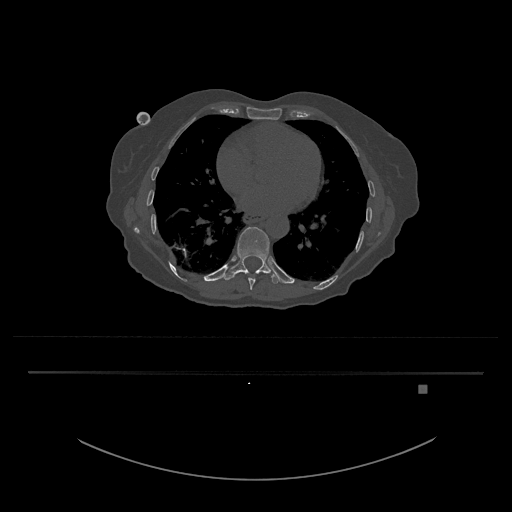
CT including the spine, one axial slice; position 730 of 797 along the scan axis; reconstruction kernel Br40s/3; 120 kVp; bone window (W 1800 / L 400 HU); 0.5 mm slice thickness; 512 × 512 image matrix, field of view 500 × 500 mm. Female patient, age 57 years. Case-level facts recorded for this patient, not image findings: primary cancer: cervical.
Annotated regions visible in this slice (semi-automatically segmented with operator editing):
- T10 vertebra: bounding box (x1, y1, x2, y2) in pixels: (223, 227, 282, 284)
- T9 vertebra: (248, 278, 255, 290)